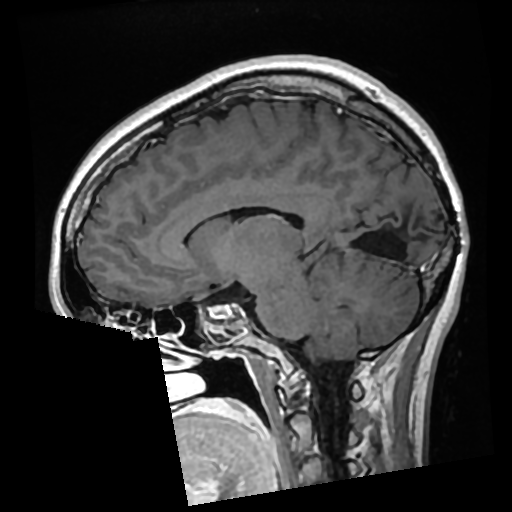
Brain MRI from a brain-tumour surgery series, one sagittal slice. Position 126 of 276 along the scan axis. T1-weighted post-contrast. 512 × 512 image matrix, field of view 250 × 250 mm. Case-level facts recorded for this patient, not image findings: histopathology: Glioma with ependymal features; WHO grade: 2; tumour location: Left Parietal.
Annotated regions visible in this slice (manually delineated by an expert):
- previous resection cavity: bounding box (x1, y1, x2, y2) in pixels: (394, 247, 400, 251)